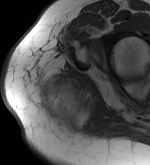
MRI of an extremity soft-tissue mass, one axial slice; slice 40 of 56 in the series (ordered by position); MR volume resampled by the dataset authors to the PET/CT grid (not the native acquisition matrix); 3.27 mm slice thickness; 150 × 165 image matrix. Female patient. From the clinical record (not read from this slice): histological type: epithelioid sarcoma with vascular differentiation; site of the primary tumour: right buttock.
Outlined on this slice (expert contour drawn on MRI and transferred to this co-registered scan by the dataset authors):
- gross tumour volume (mass): bounding box [x1, y1, x2, y2] px = [37, 74, 97, 126]